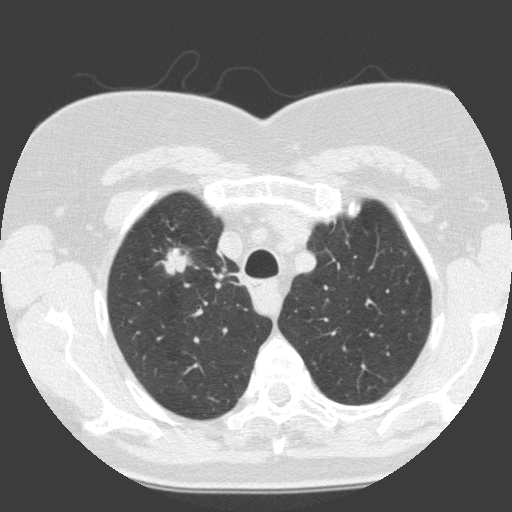
Low-dose screening chest CT, one axial slice. Position 118 of 146 along the scan axis. 120 kVp. Lung window (W 1500 / L -600 HU). 2 mm slice thickness. 512 × 512 image matrix, field of view 300 × 300 mm.
Outlined on this slice (manually delineated by an expert):
- lesion 1 (tumor, upper lobe of right lung): bounding box (x1, y1, x2, y2) in pixels: (158, 248, 192, 275)